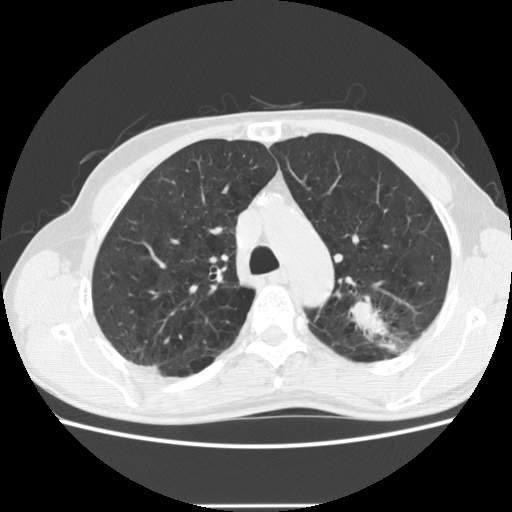
Axial slice from a low-dose chest CT screening exam, baseline screening round, lung window (W 1500 / L -600 HU), 2.5 mm slice thickness. Male participant, aged 64 years at enrolment.
Expert-annotated lung lesion, box from (x=339, y=281) to (x=440, y=361) px. The exam's reader record, not a measurement of the box and not confirmed to be the same lesion: non-calcified nodule or mass ≥4 mm, left upper lobe, 27 × 19 mm, poorly defined margins, soft tissue attenuation. Participant outcome: lung cancer diagnosed 23 days after this screen — adenocarcinoma, NOS, left upper lobe, moderately differentiated (G2), stage IA (AJCC 6th edition), 29 mm at pathology.